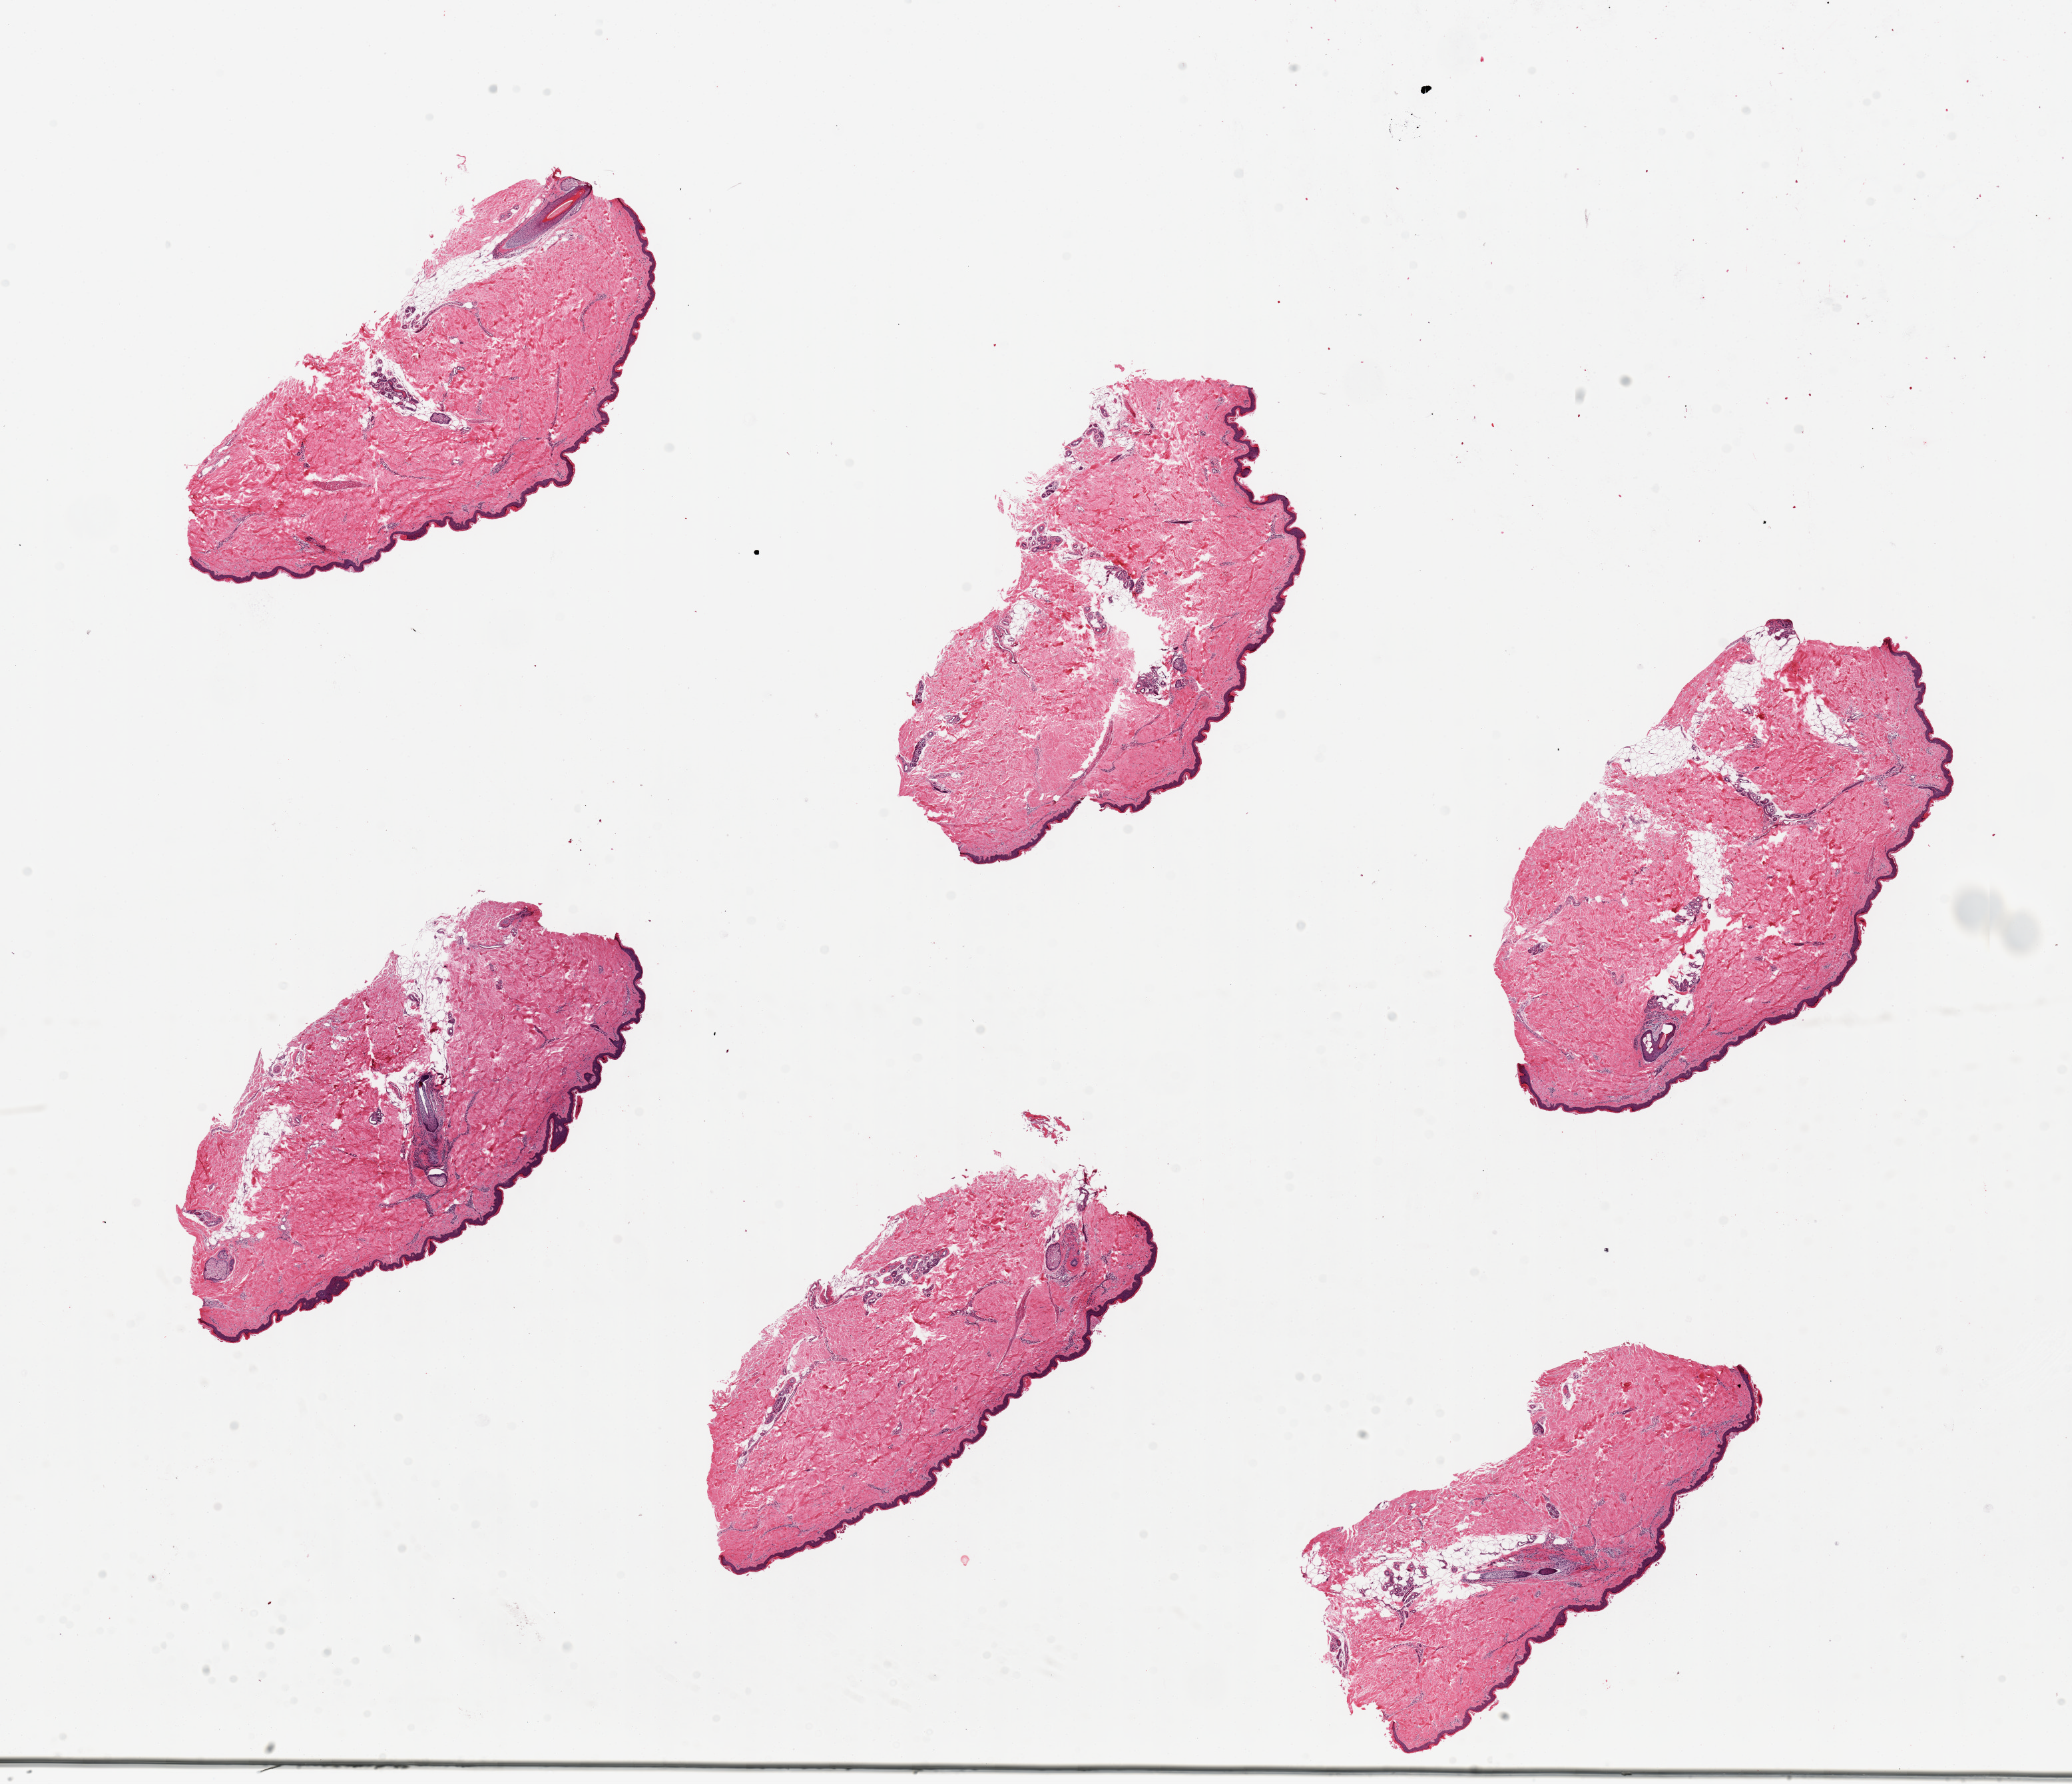
H&E whole-slide image, a low-resolution overview of the entire scanned area, about 24.6 x 21.2 mm (acquisition: 20x scan); PAXgene-fixed paraffin-embedded (PFPE) section; target tissue: skin of lower leg; tissue donor sample. Donor sex: male.
Reviewer comment on this tissue sample: 1 piece (8x3mm), correlates with2125.